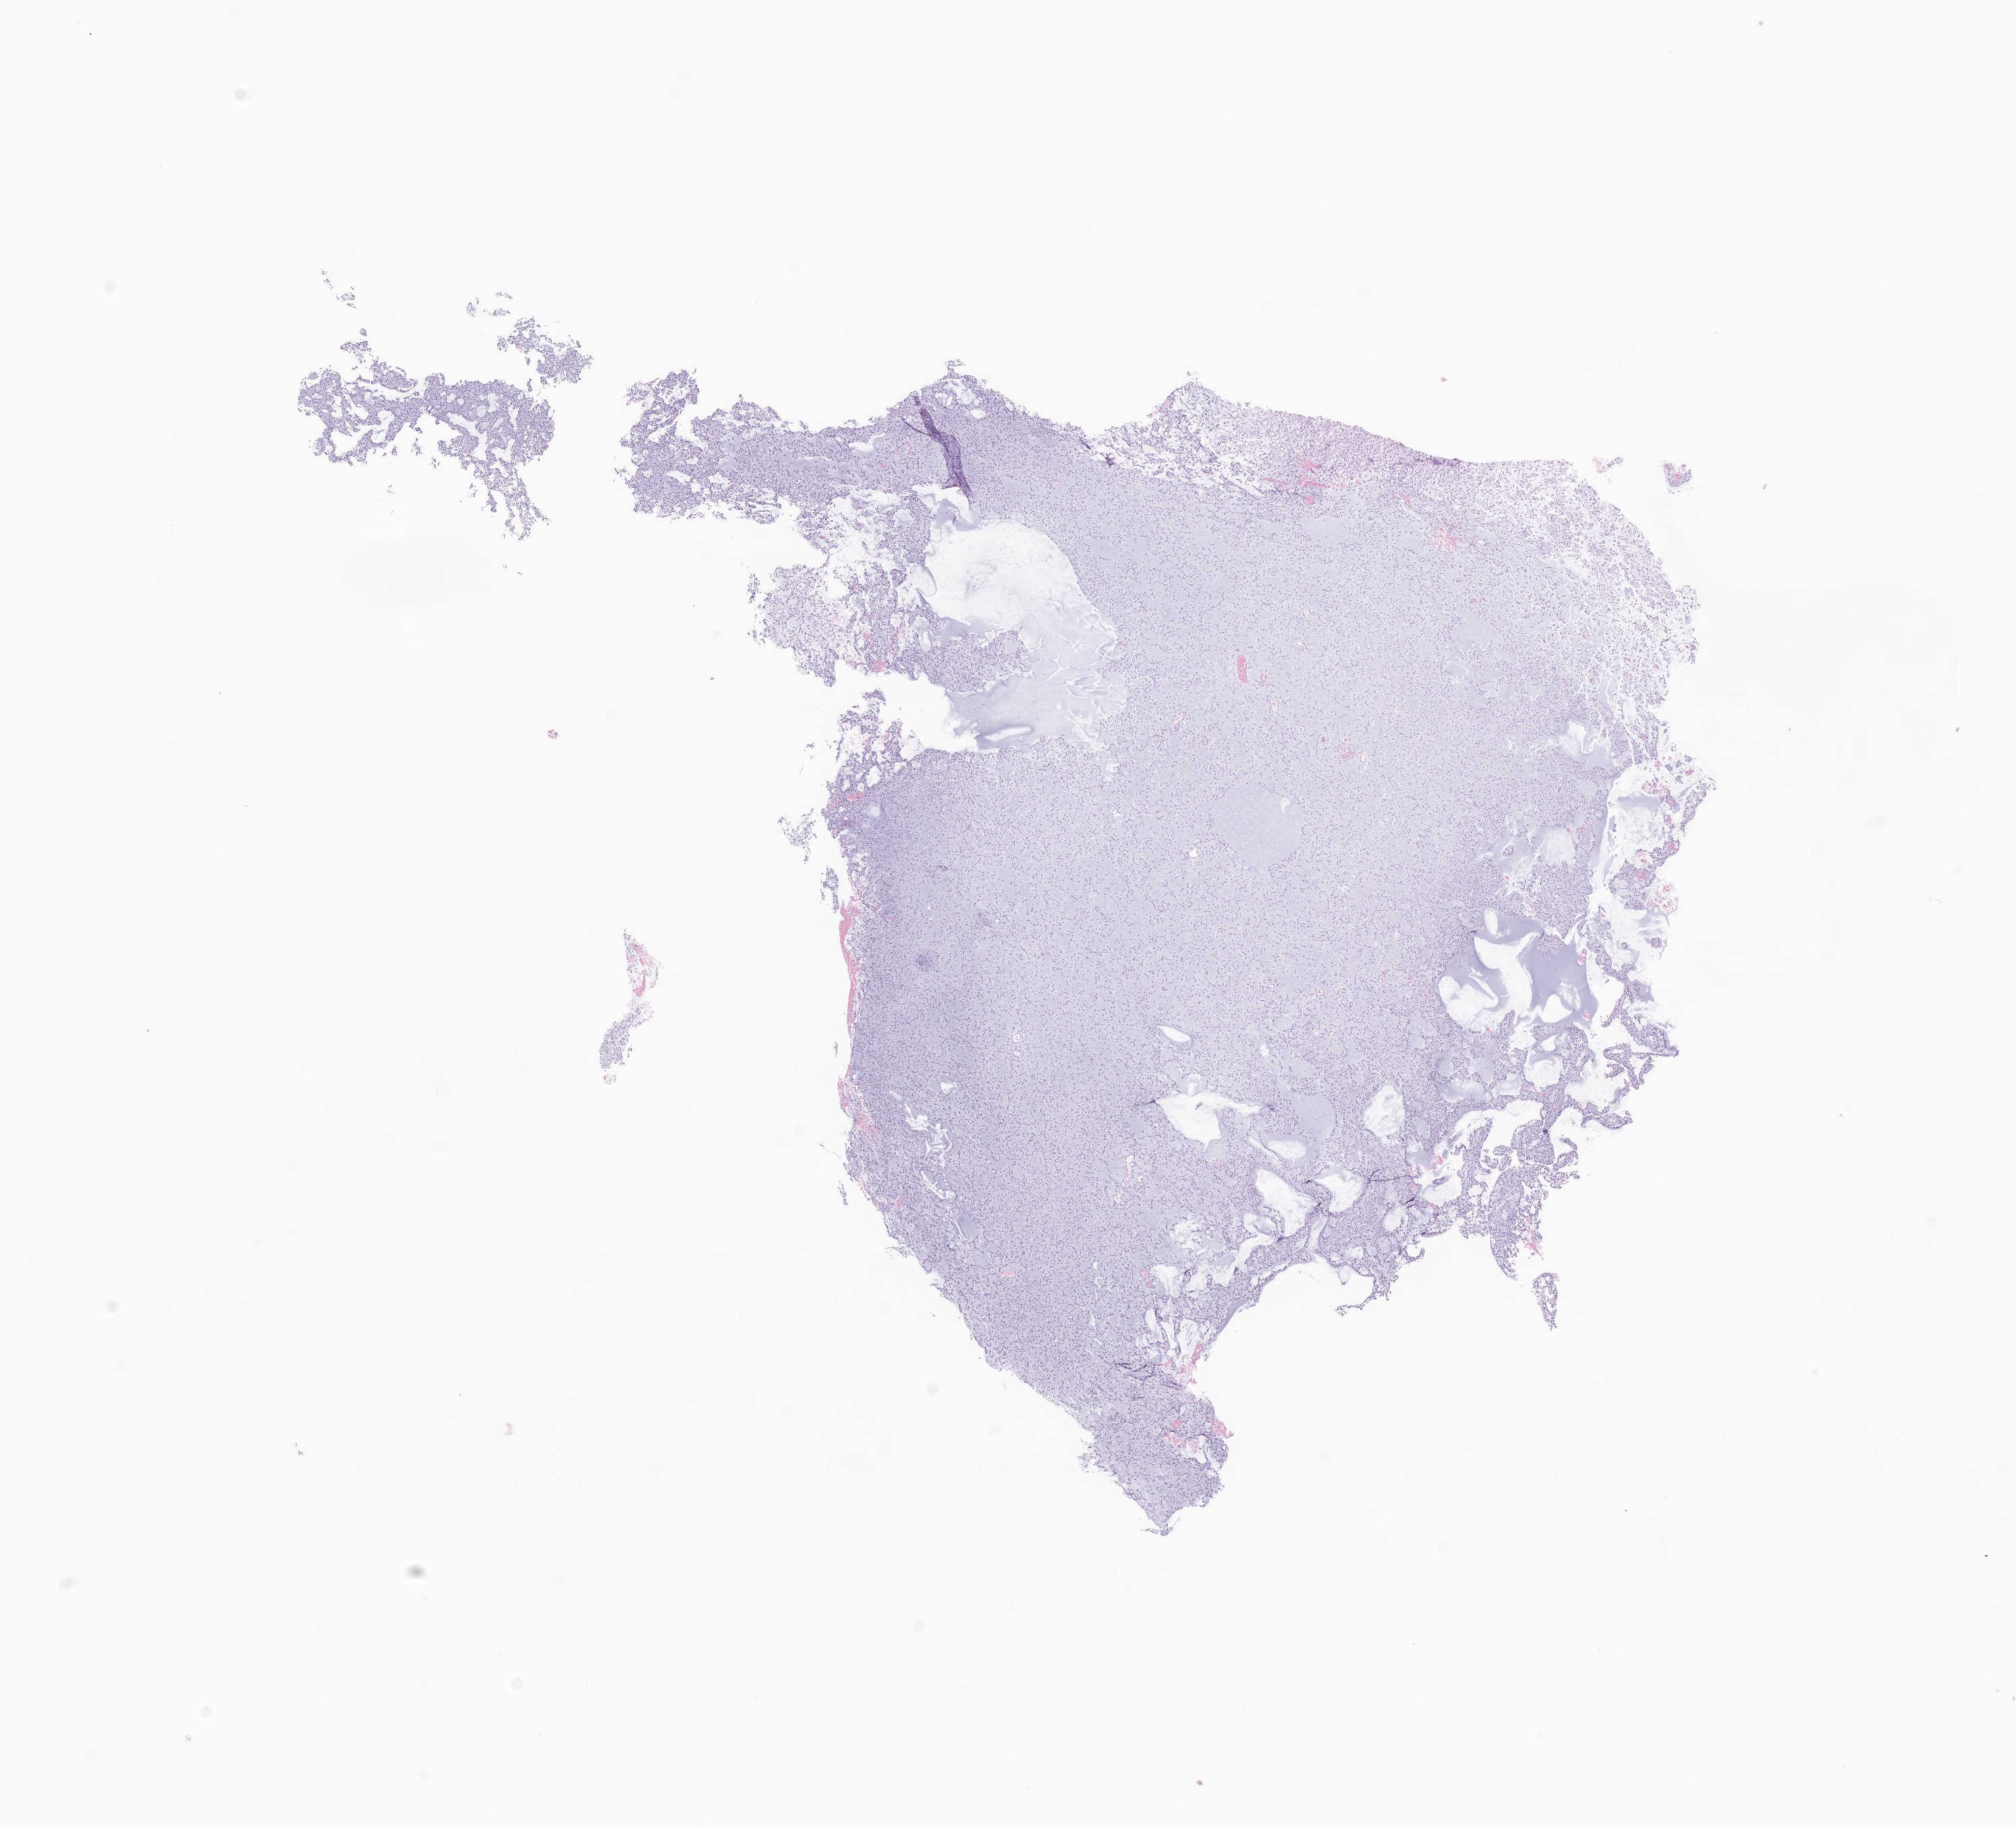
Whole-slide image, H&E stain of tumor tissue from the temporal lobe, whole scanned area (about 12.6 x 11.4 mm) shown as a low-resolution overview; formalin-fixed, paraffin-embedded (FFPE) tissue. Patient male; age 118 months (9 years 10 months).
Diagnosis: Dysembryoplastic neuroepithelial tumor.